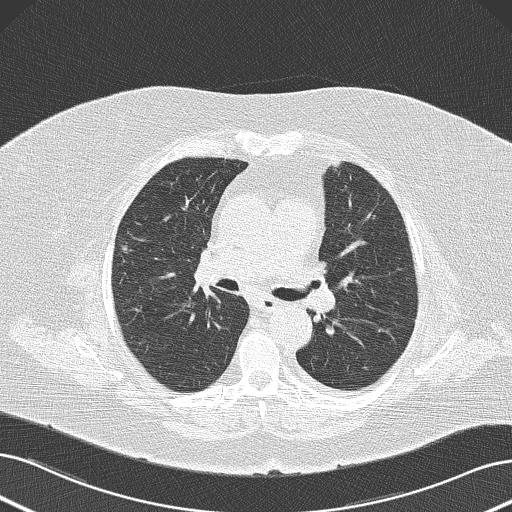
Low-dose screening chest CT, axial slice; baseline screening round; lung window (W 1500 / L -600 HU); 2 mm slice thickness; lung (sharp) reconstruction kernel (B50f); slice 65 of 145 in the series; 512 × 512 image matrix. Female, age 73 years at enrolment. Former smoker at enrolment.
- Expert-annotated lung lesion, bounding box <105,223,151,263> (left, top, right, bottom; pixels).
- Screening reader's record for this exam (one nodule recorded; not confirmed to be the boxed lesion): non-calcified nodule or mass ≥4 mm, right upper lobe, 15 × 11 mm, poorly defined margins, soft tissue attenuation.
- Official screen result: positive, change unspecified: nodule(s) >= 4 mm or enlarging nodule(s), mass(es), or other non-specific abnormalities suspicious for lung cancer.
- Lung cancer was diagnosed 55 days after this screen: neoplasm, malignant, right upper lobe, stage IA (AJCC 6th edition), 15 mm at pathology.